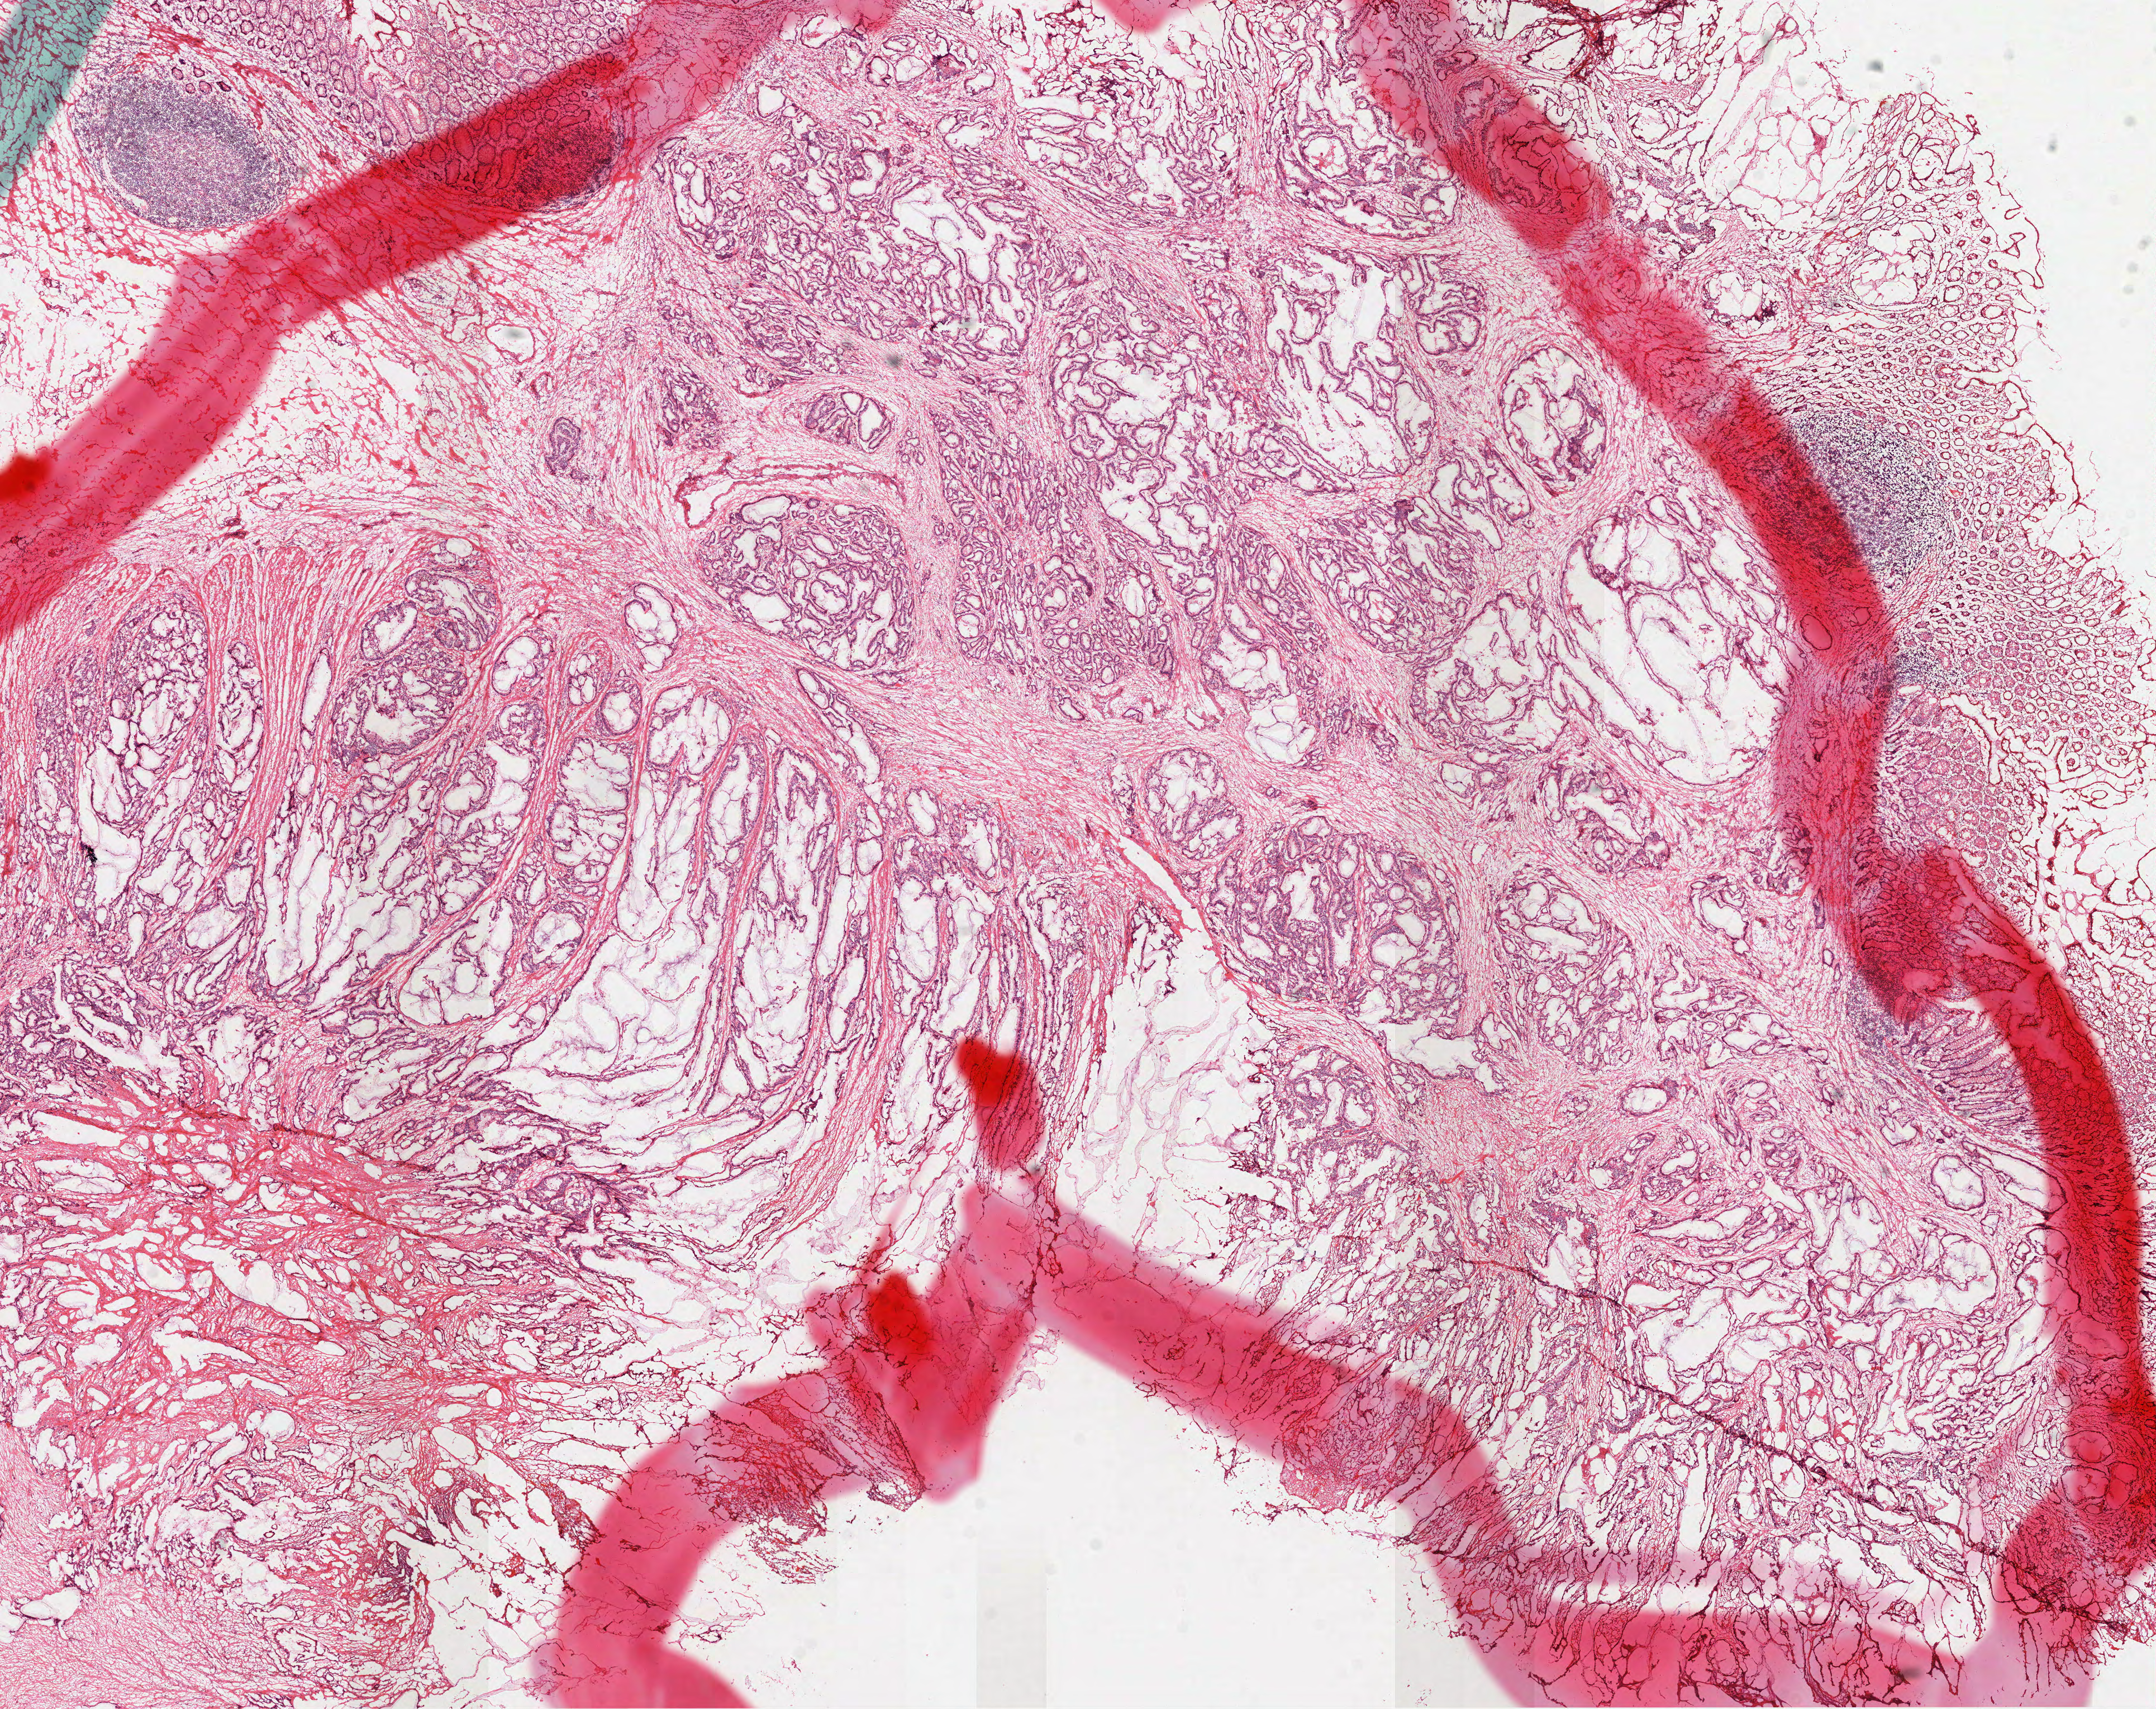
Digitized Hematoxylin and eosin (H&E) stained tissue section (whole slide), shown as a low-resolution overview of the whole scanned area (about 15.6 x 12.3 mm), frozen section, sample: primary tumour, colon. Patient: female, age at initial diagnosis 41 years. Pathologist review of this section (percent, as recorded): tumour cells 98%, tumour nuclei 85%.
Diagnosis: Adenocarcinoma, NOS.